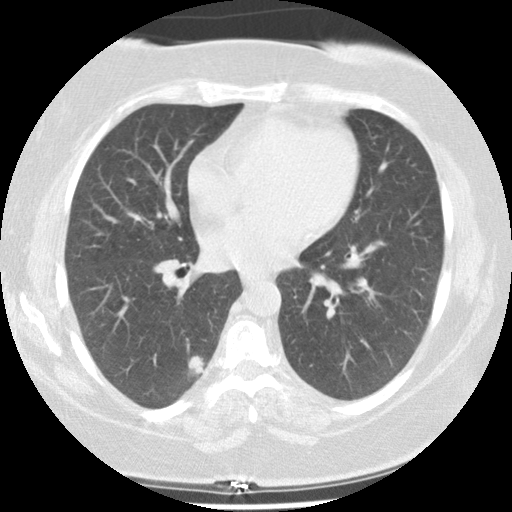
Low-dose screening chest CT, one axial slice; slice 73 of 131 in the series (ordered by position); reconstruction kernel STANDARD; lung window (W 1500 / L -600 HU); 512 × 512 image matrix.
Outlined on this slice (expert manual segmentation):
- lesion 1 (tumor, lower lobe of right lung): bounding box <188,345,204,374> (left, top, right, bottom; pixels)